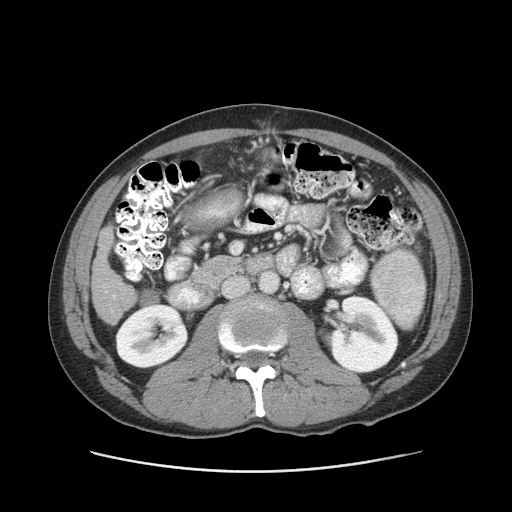
Contrast-enhanced abdominal CT (liver protocol), one axial slice; position 30 of 93 along the scan axis; 120 kVp; soft-tissue window (W 400 / L 40 HU); 2.5 mm slice thickness; 512 × 512 image matrix. Case-level facts recorded for this patient, not image findings: diagnosis: hepatocellular carcinoma (patient treated with transarterial chemoembolisation; whether this scan precedes or follows treatment is not stated here); TNM stage (as recorded): Stage-II; Child-Pugh class: A; tumour differentiation: moderately differentiated; tumour nodularity: multinodular.
Structures marked on this image (semi-automatic segmentation, software-assisted and operator-edited):
- liver parenchyma outside the tumour (the mass and vessels are separate outlines, so this box may not span the whole liver): bounding box [x1, y1, x2, y2] px = [92, 226, 135, 324]